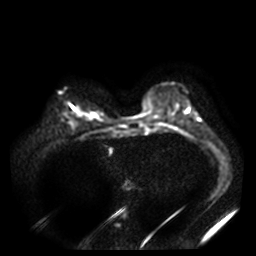
Breast MRI, one axial slice; slice 12 of 40 in the series (ordered by position); diffusion-weighted series; image 2 of 4 stored at this slice position (different b-values; order by instance number); 3 T; 5 mm slice thickness; 256 × 256 image matrix. Female patient.
Annotated regions visible in this slice (outlined manually by an expert reader):
- tumour on diffusion-weighted imaging: bounding box (x1, y1, x2, y2) in pixels: (74, 109, 80, 115)